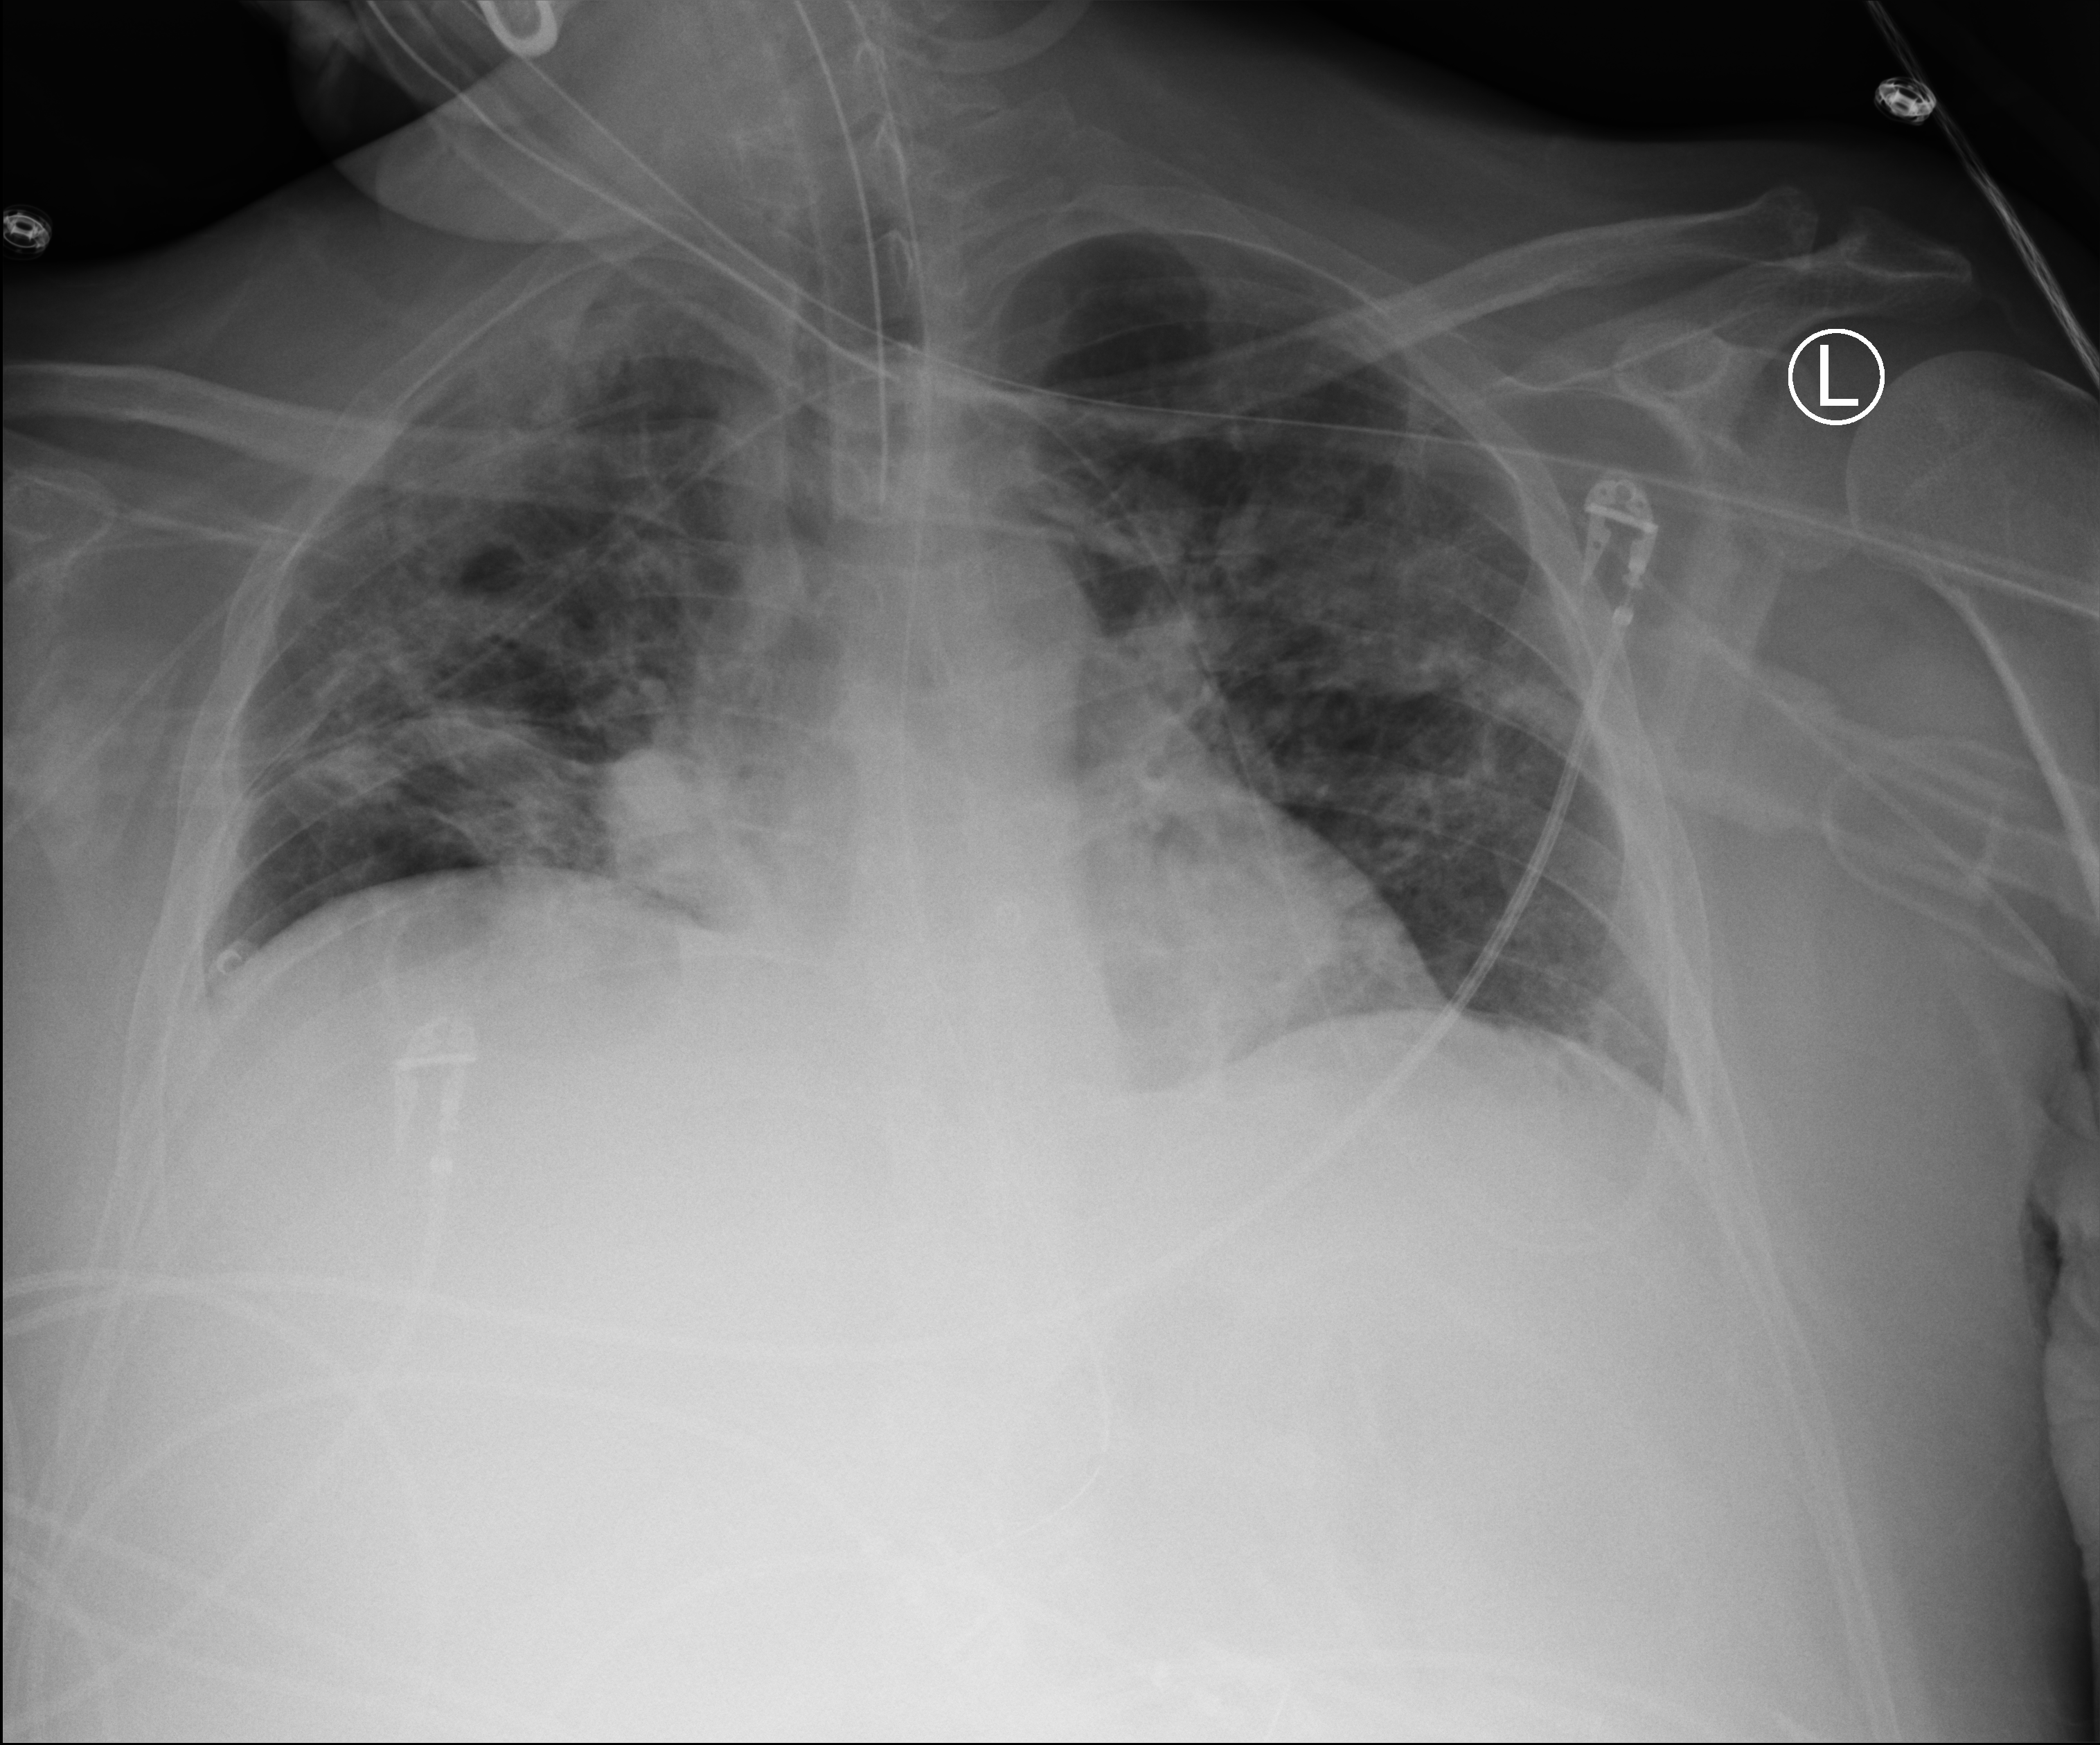
Bedside chest radiograph (computed radiography), anteroposterior (AP) projection. Adult patient hospitalised with COVID-19, age 18–59 years.
Admission-level facts for this patient (not findings on this image; timing relative to this image not recorded):
- admitted to intensive care during this hospital stay: yes